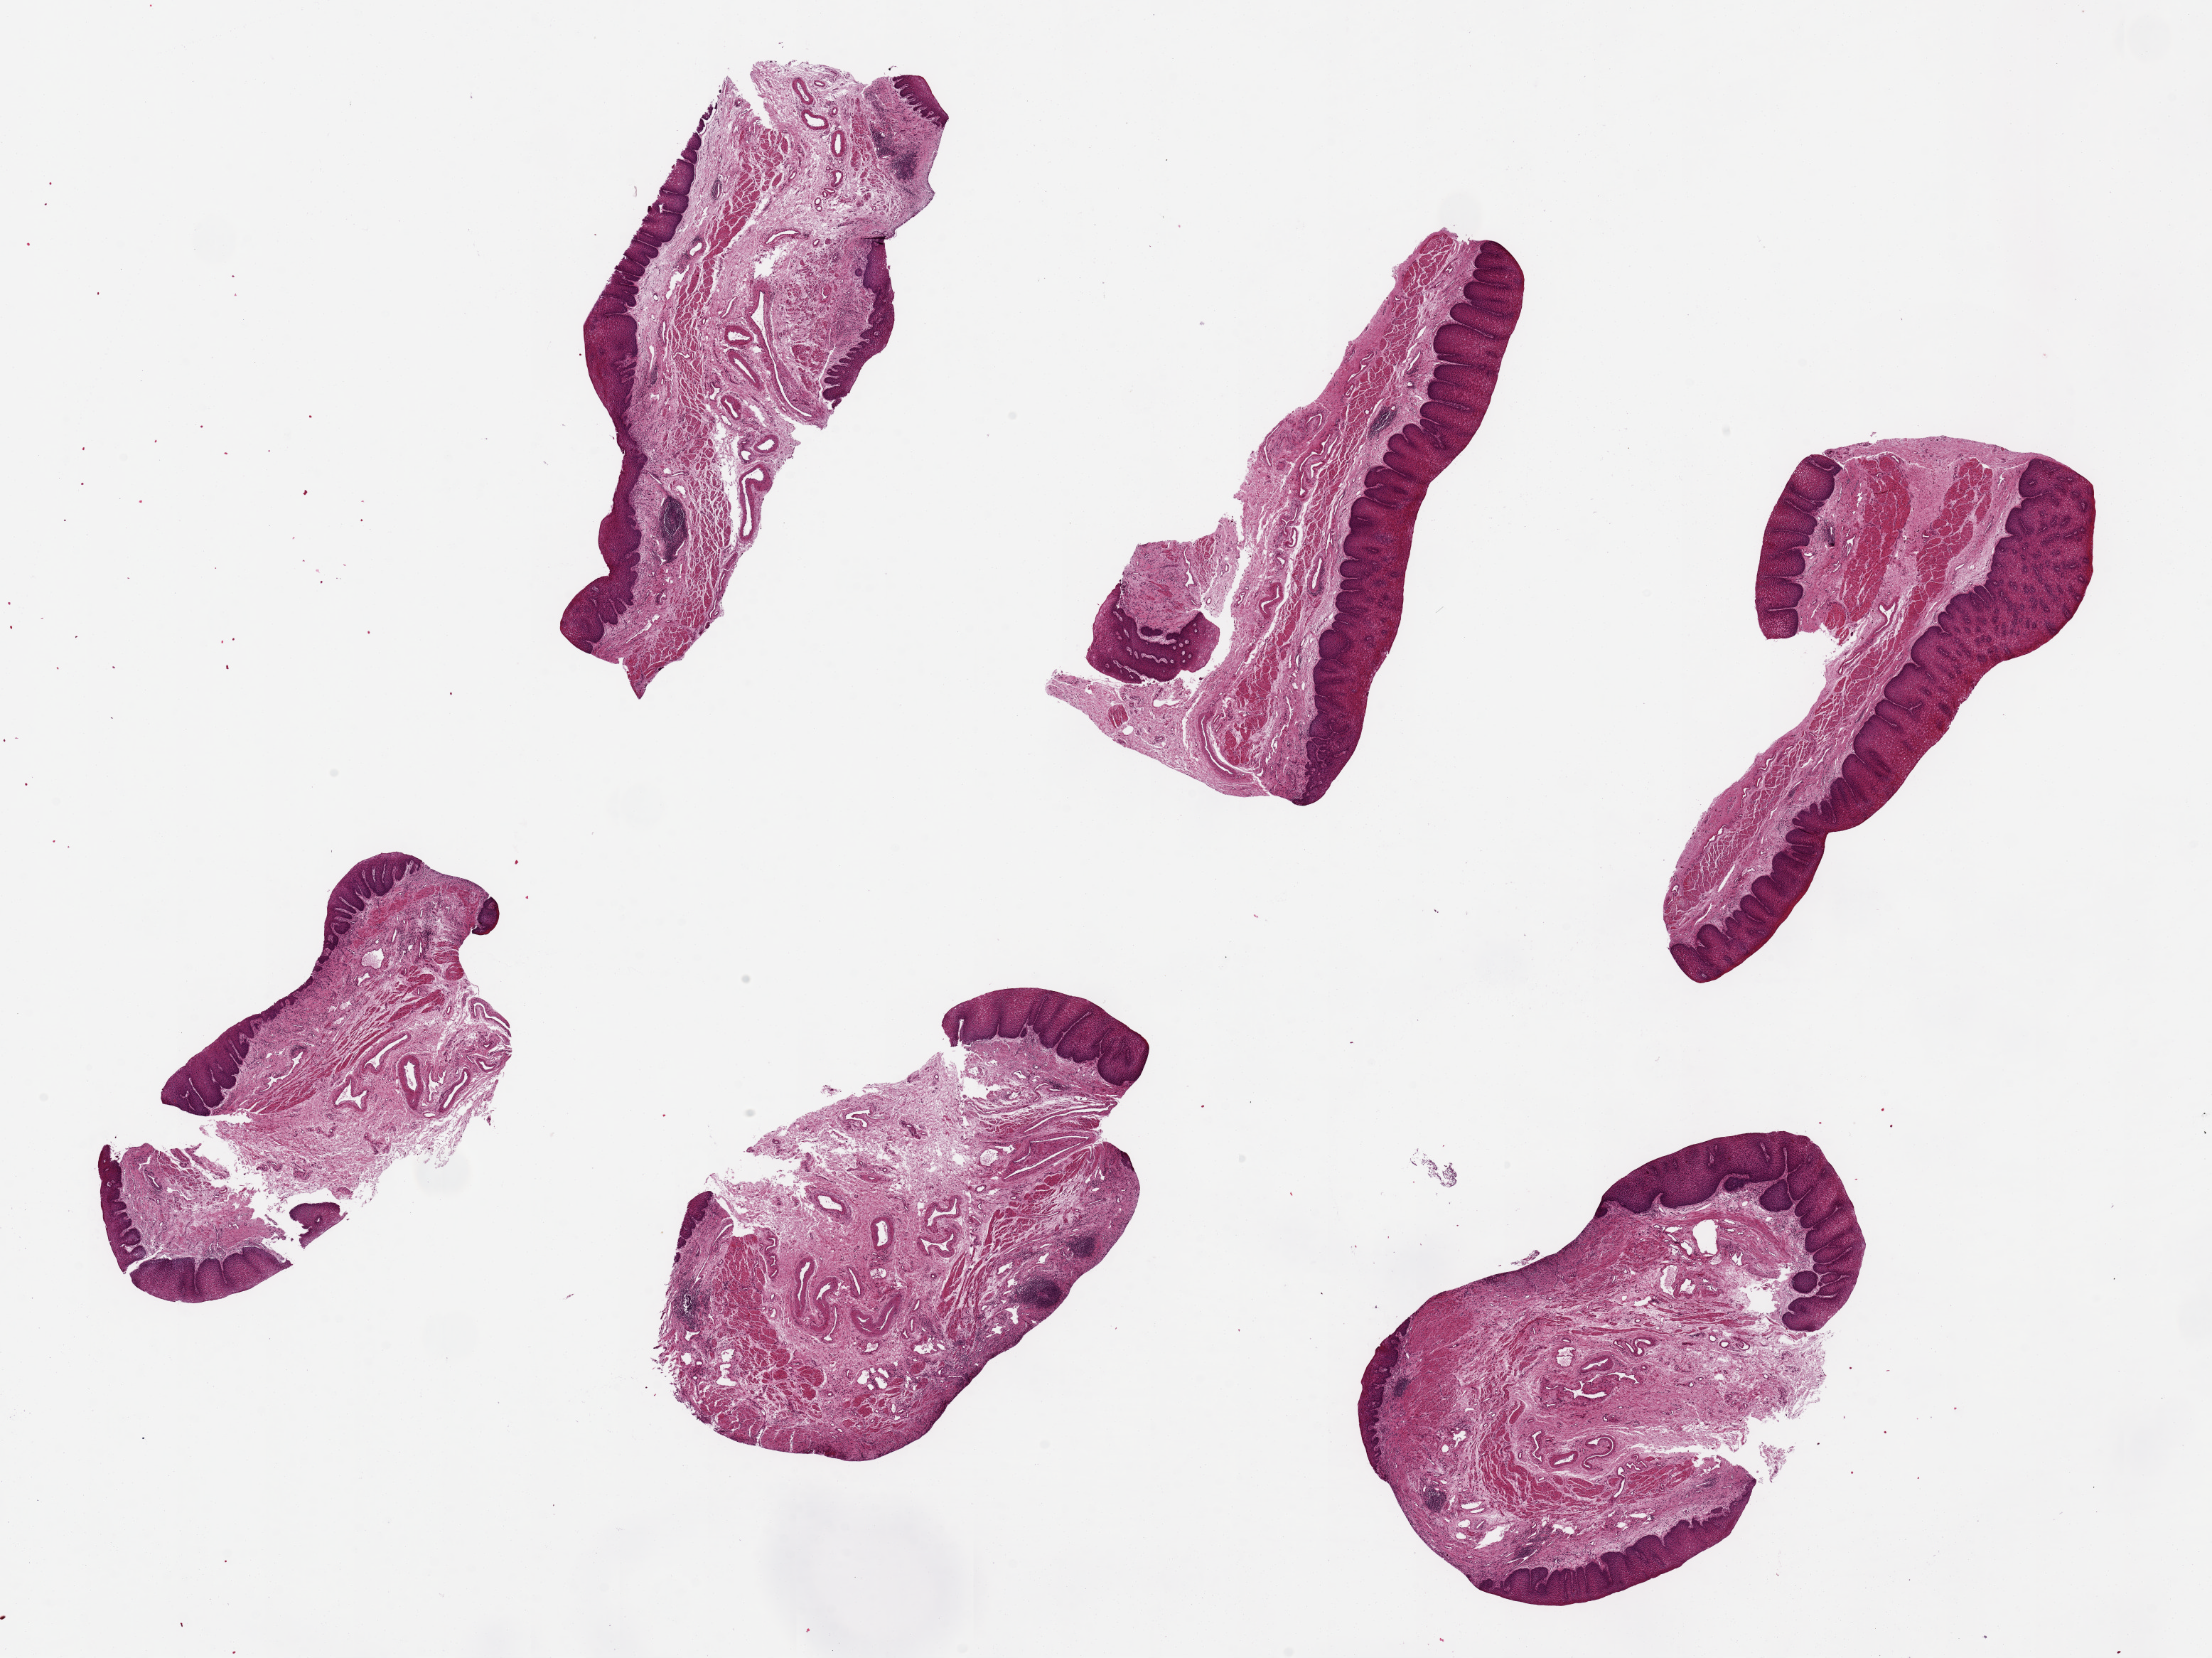
Digitized haematoxylin and eosin-stained section, a low-resolution overview of the entire scanned area, about 24.6 x 18.4 mm. PAXgene-fixed, paraffin-embedded tissue. Section of esophageal mucous membrane (target tissue). Tissue donor sample.
Pathologist's review note for this sample: 6 pieces up to 7x4 mm; all have mucosa, no muscularis propria.